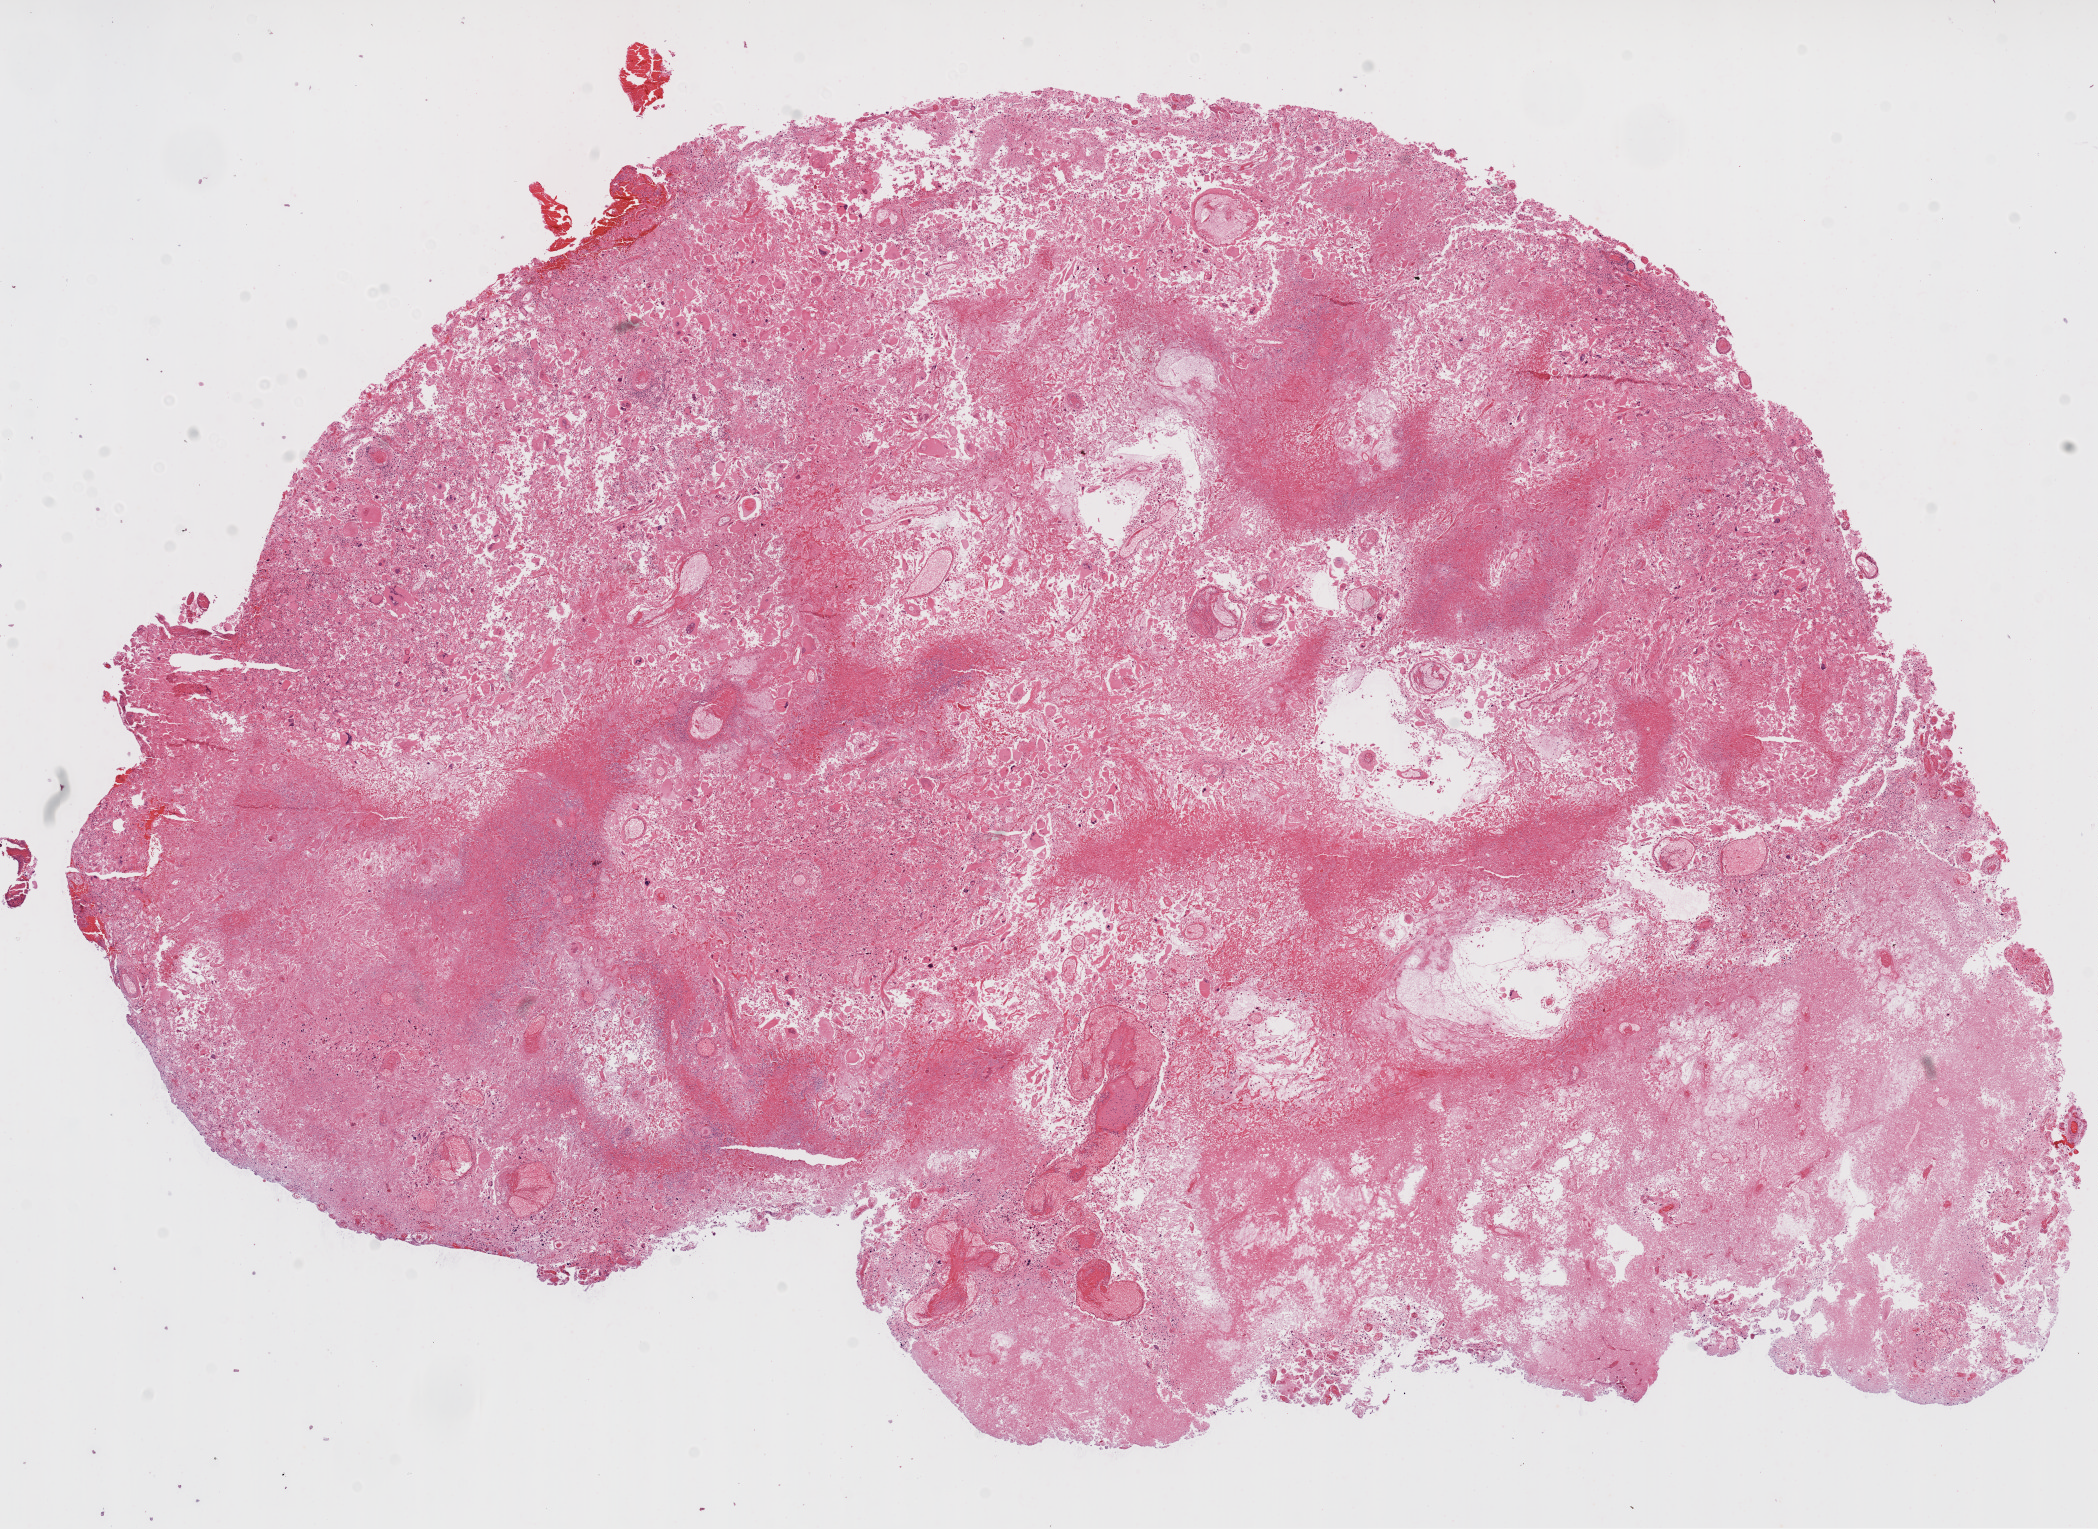
Whole-slide histology image, H&E — shown as a low-resolution overview of the whole scanned area (about 16.9 x 12.3 mm, acquisition: 20x scan); formalin-fixed paraffin-embedded (FFPE) diagnostic section; primary tumour sample from the brain. Patient: female, age at initial diagnosis 55 years.
• pathologic diagnosis: Glioblastoma